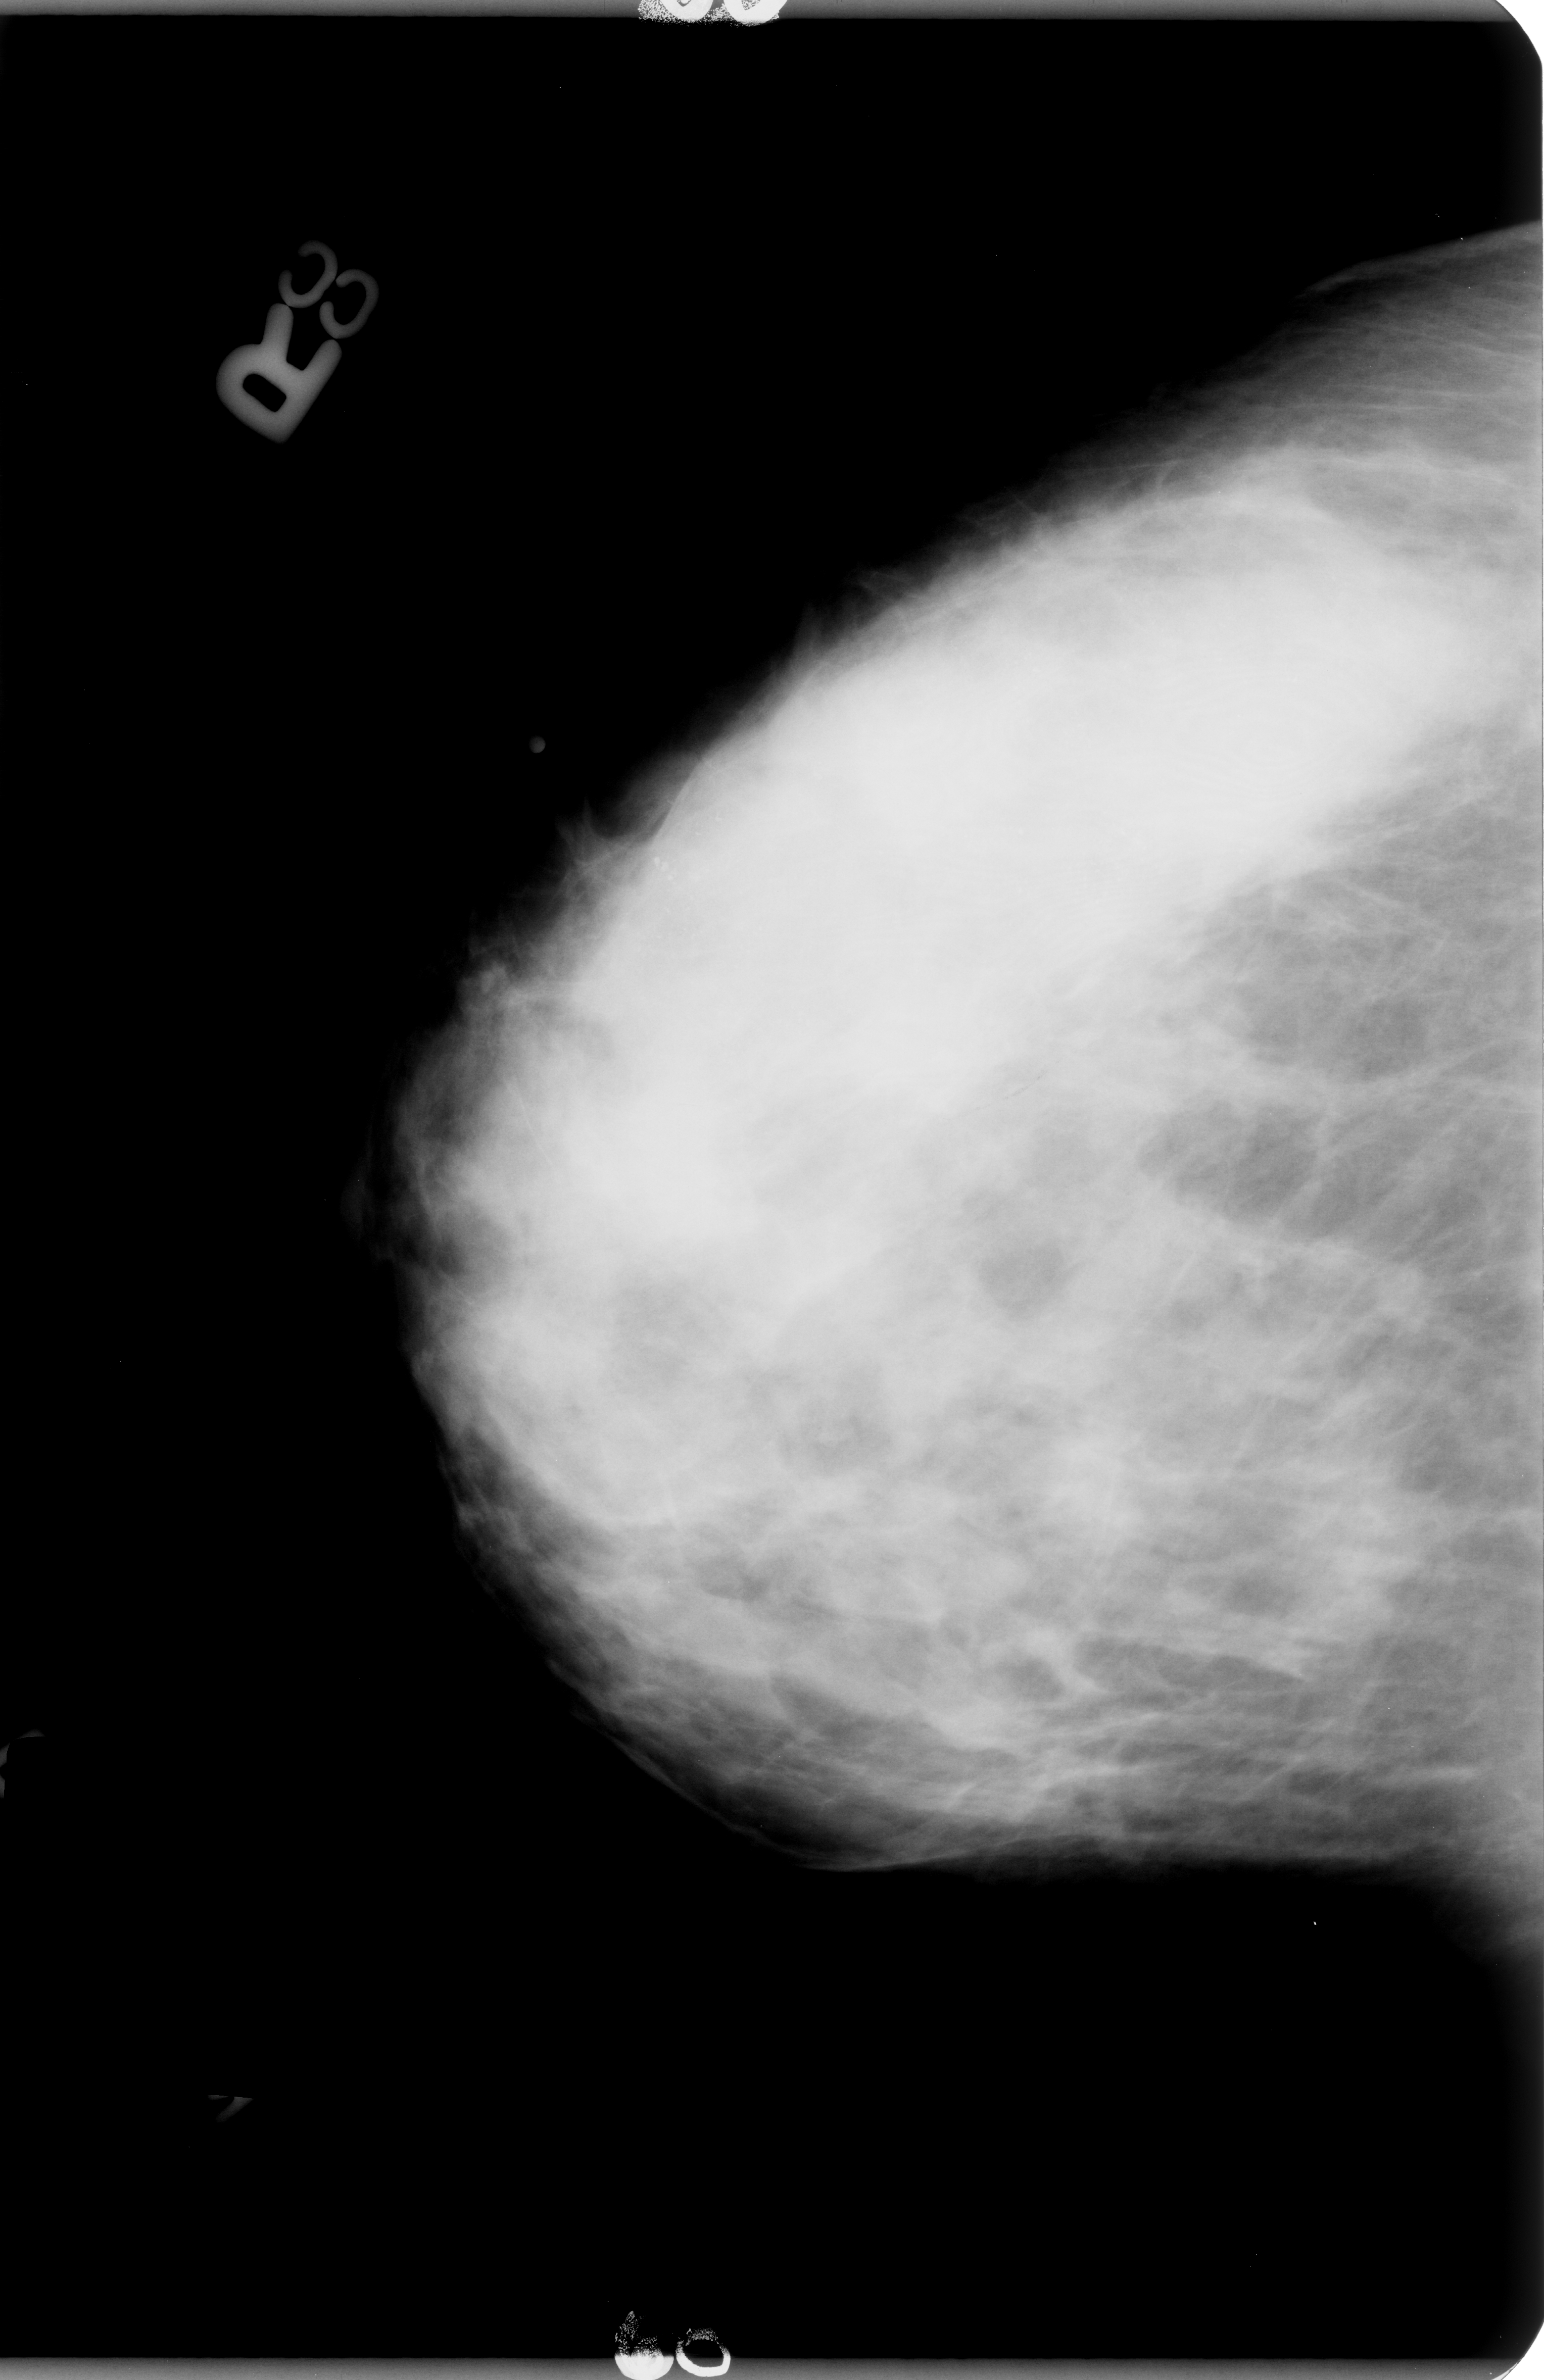
Scanned film-screen mammogram, right breast, craniocaudal (CC) view, breast composition: heterogeneously dense (BI-RADS density category 3 of 4).
Radiologist-marked abnormalities on this image: calcifications, morphology pleomorphic, distribution regional; BI-RADS assessment category 4; subtlety rating 3 on a 1 (subtle) to 5 (obvious) scale; pathology result (as recorded, not read from the image): malignant.